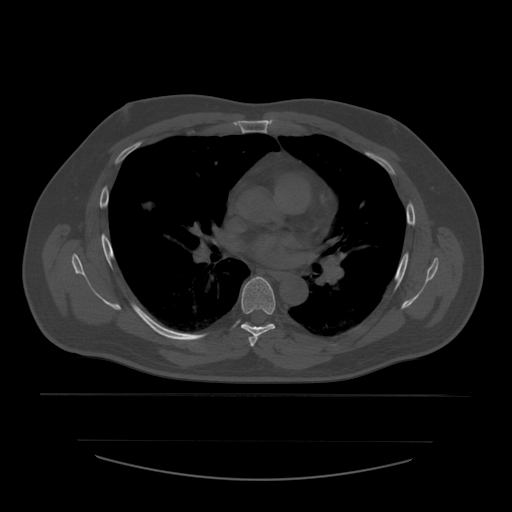
CT including the spine, one axial slice; position 377 of 532 along the scan axis; 120 kVp; bone window (W 1800 / L 400 HU); 512 × 512 image matrix, field of view 441 × 441 mm. Patient age 44 years. Case-level facts recorded for this patient, not image findings: primary cancer: soft tissue sarcoma.
Outlined on this slice (semi-automatically segmented with operator editing):
- T5 vertebra: bounding box <249,335,258,347> (left, top, right, bottom; pixels)
- T6 vertebra: <241,277,276,338>